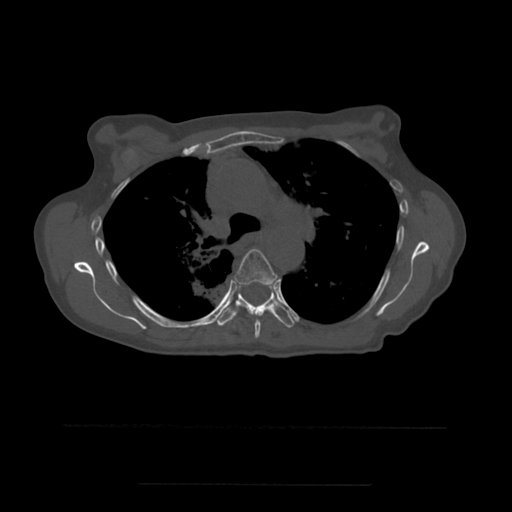
CT including the spine, one axial slice; bone window (W 1800 / L 400 HU); 512 × 512 image matrix, field of view 350 × 350 mm. Patient age 58 years. Case-level facts recorded for this patient, not image findings: primary cancer: lung.
Structures marked on this image (semi-automatically segmented with operator editing):
- T5 vertebra: bounding box [x1, y1, x2, y2] px = [235, 249, 278, 338]
- T6 vertebra: [215, 285, 295, 328]